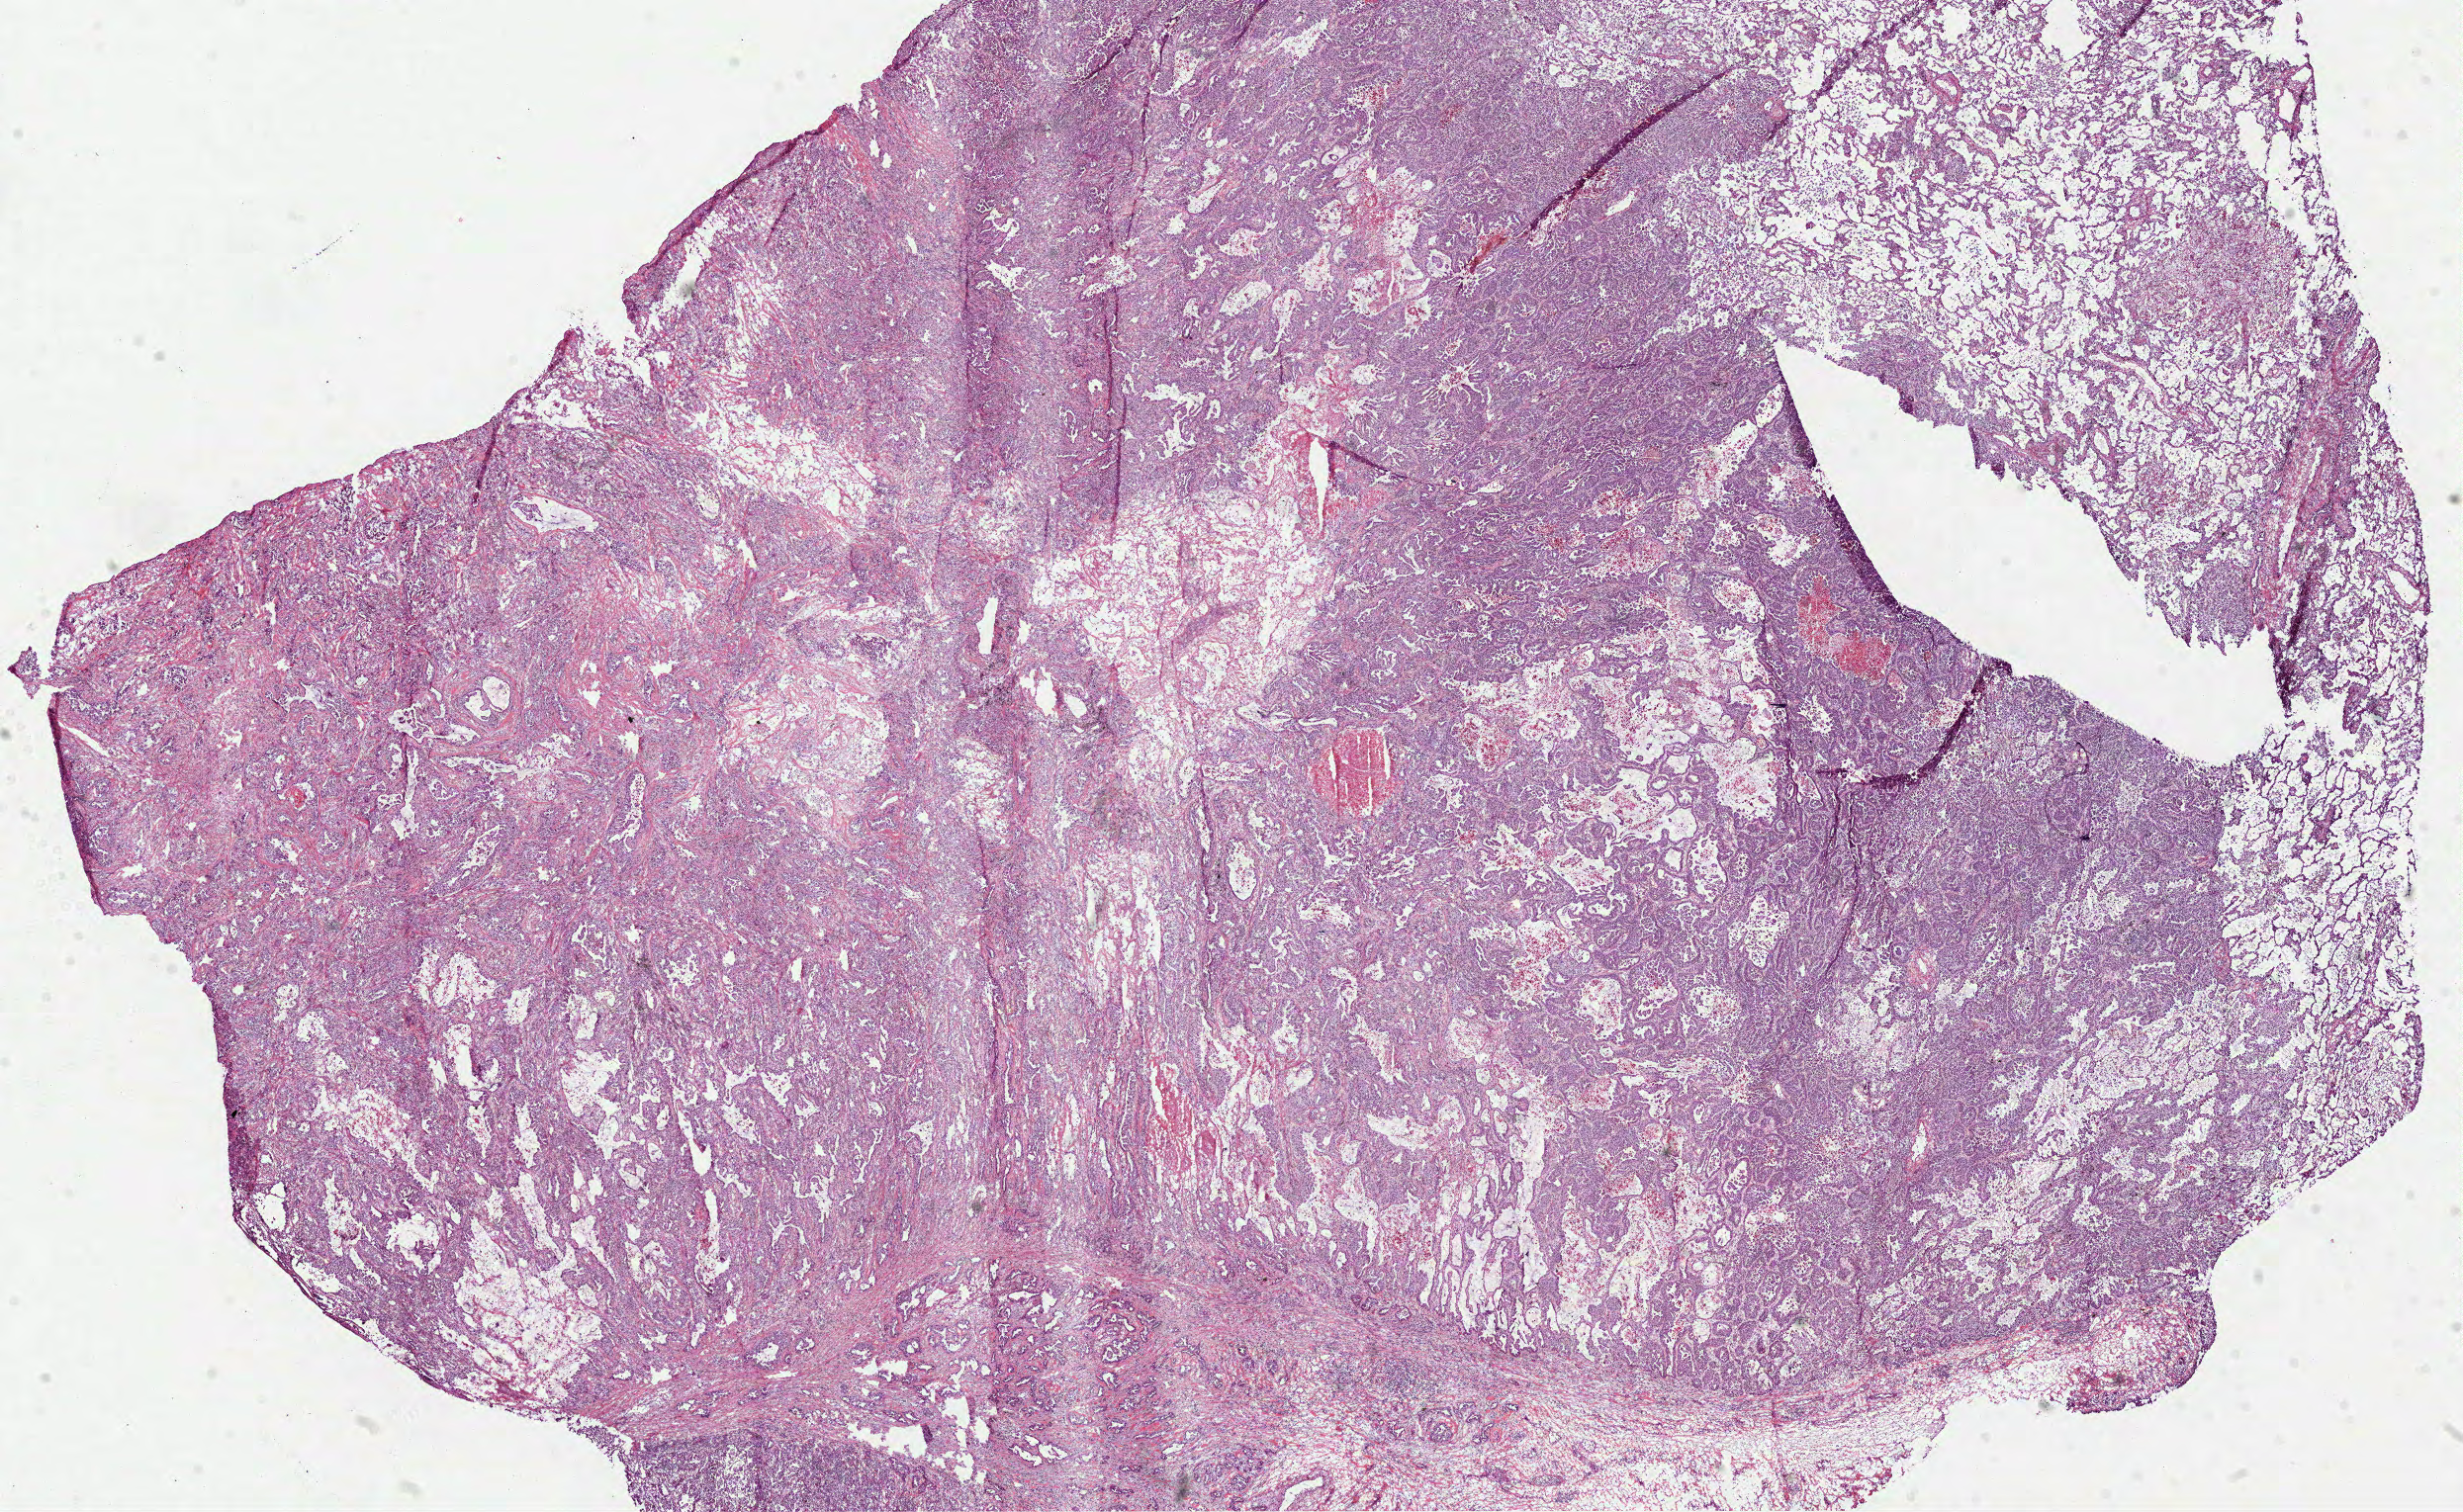
Whole-slide histology image, H&E-stained, shown as a low-resolution overview of the whole scanned area (about 20.1 x 12.3 mm), frozen section from the bottom of the tissue portion, primary tumour sample from the lung. Male, age 52 years at initial diagnosis. Composition of this section per pathologist review: tumour cells 67%, tumour nuclei 75%, normal cells 10%, stromal cells 15%, necrosis 8%.
* TNM: T2a N1 M0
* histologic diagnosis: Adenocarcinoma, NOS (upper lobe, lung)
* AJCC pathologic stage: IIA